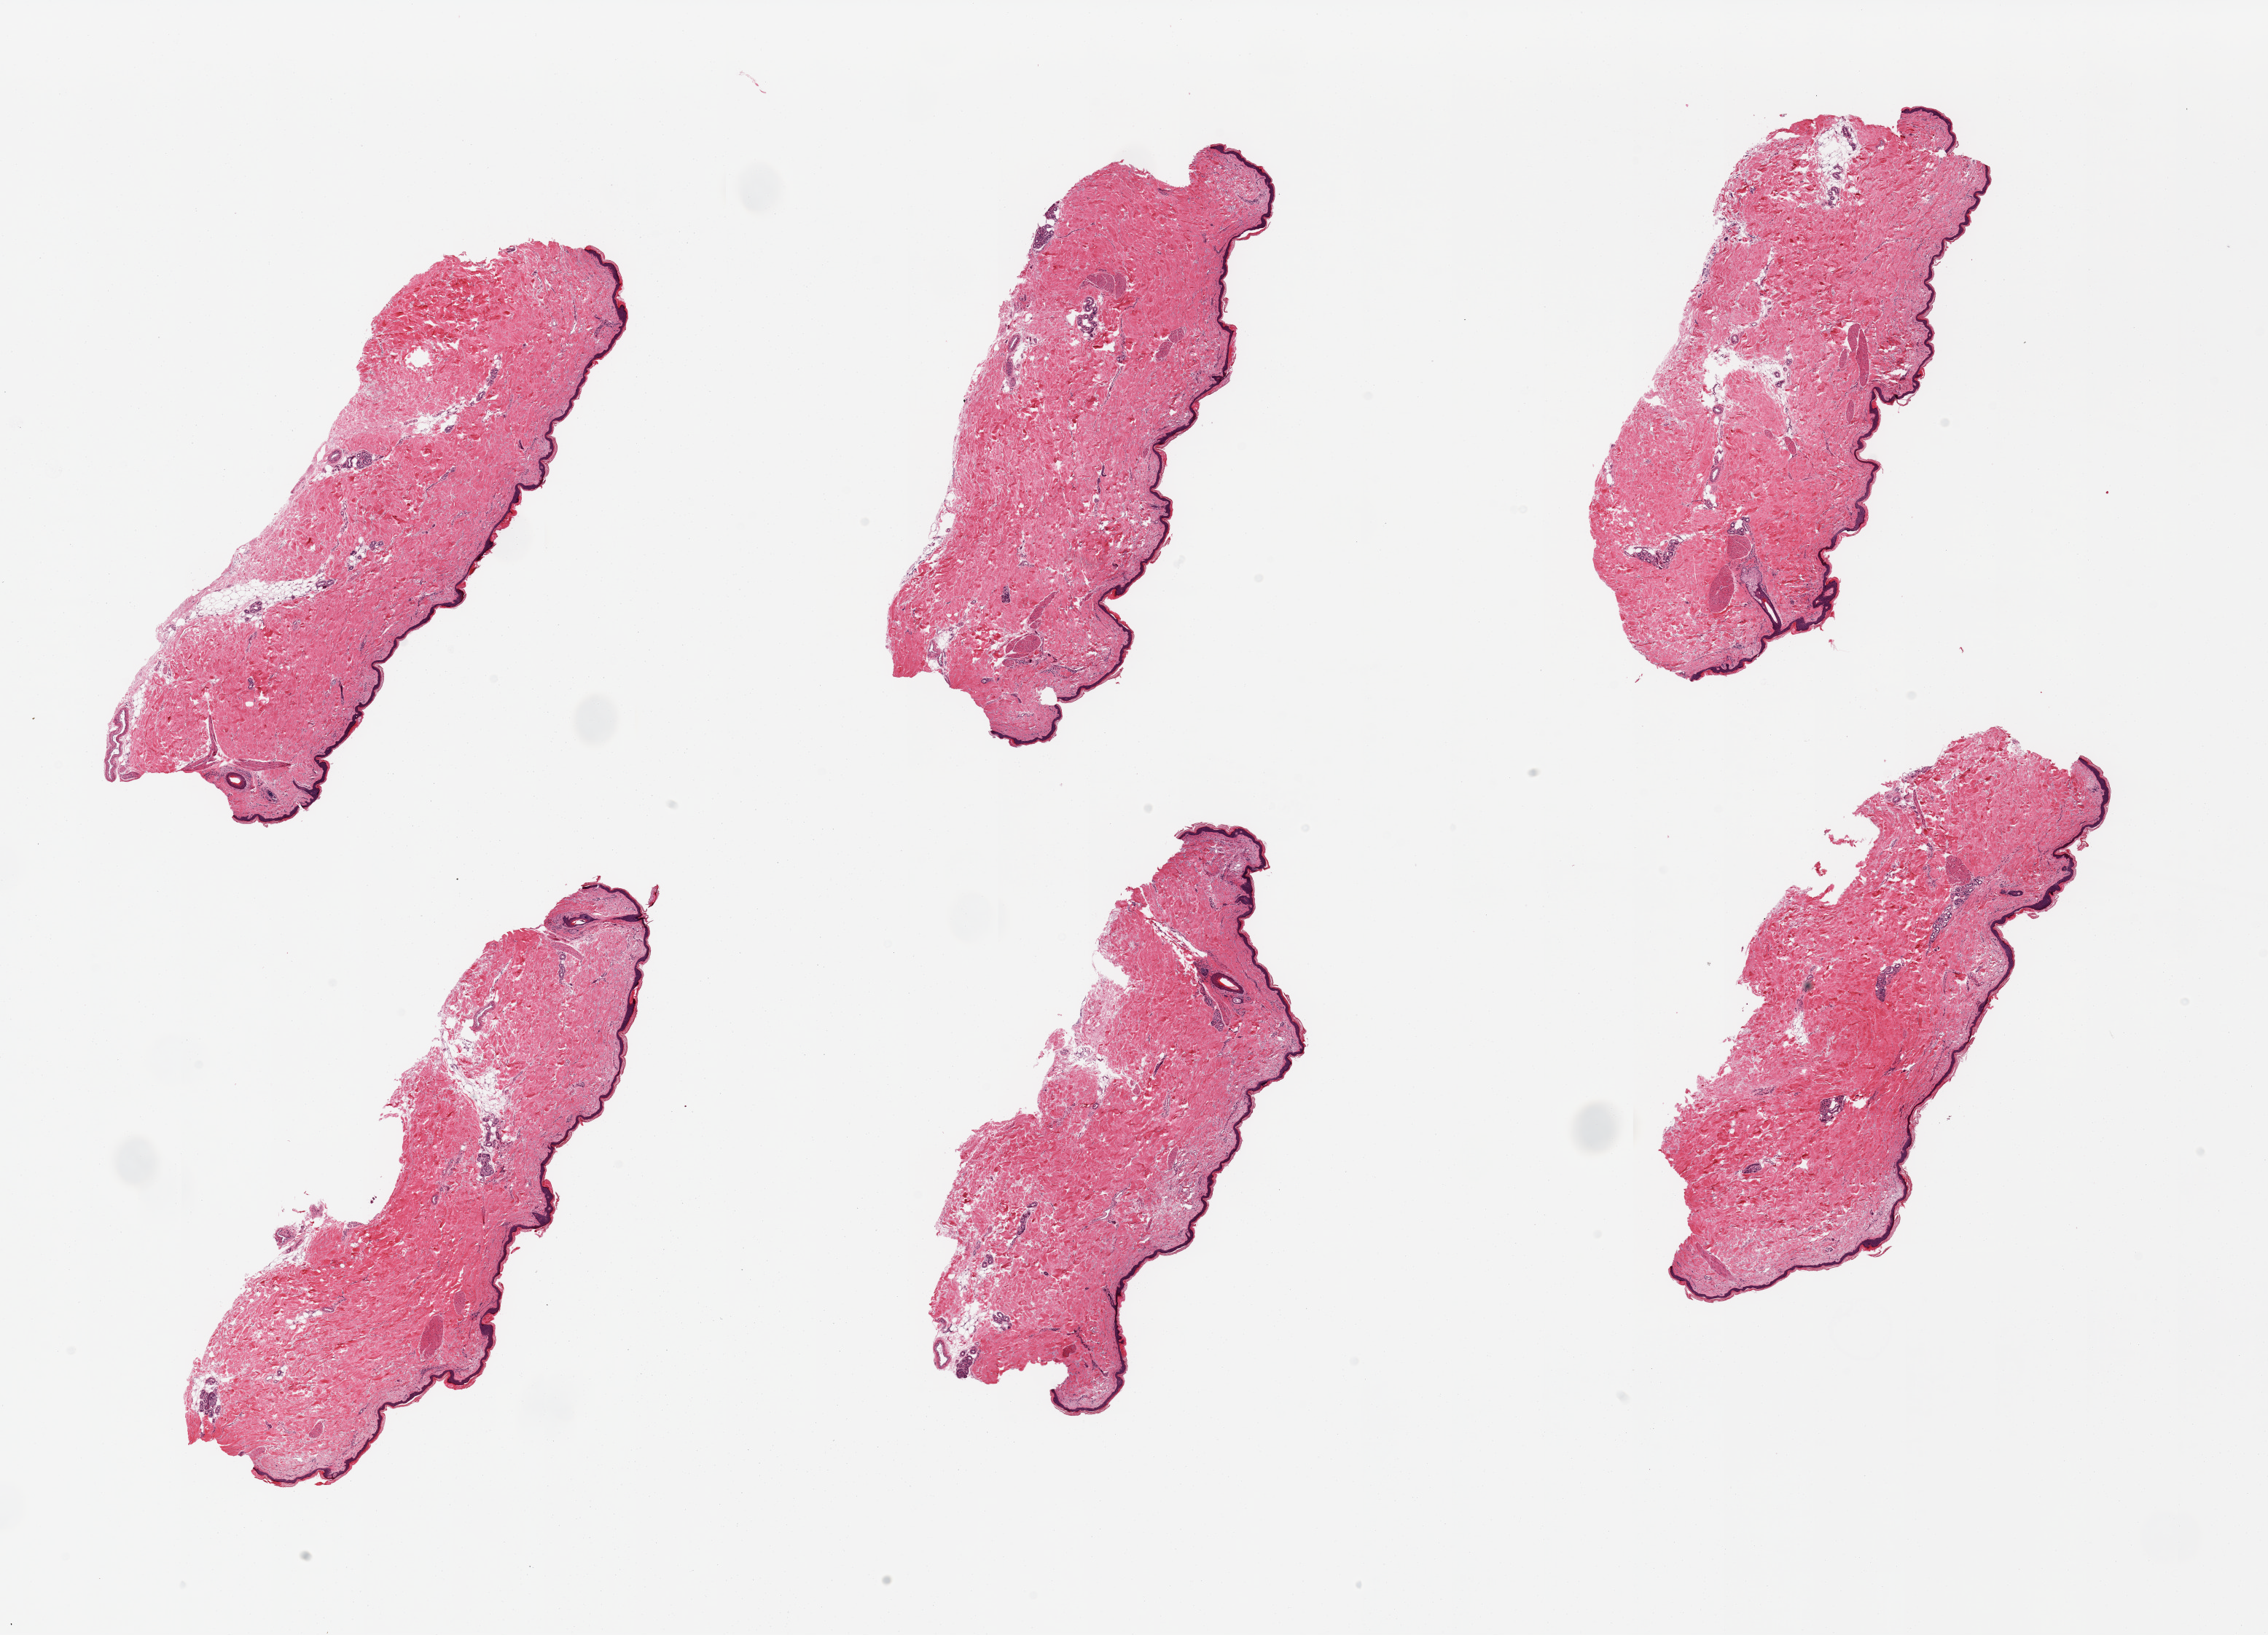
Hematoxylin and eosin (H&E) whole-slide image, brightfield — a low-resolution overview of the entire scanned area, about 24.6 x 17.7 mm (acquisition: 20x scan). PAXgene-fixed, paraffin-embedded tissue. Sampled site (target tissue): skin of lower leg. Donor tissue sample. Male donor.
Pathologist's review note for this sample: 6 pieces; minimal internal (periadnexal) fat; squamous epithelium is up to ~30um.